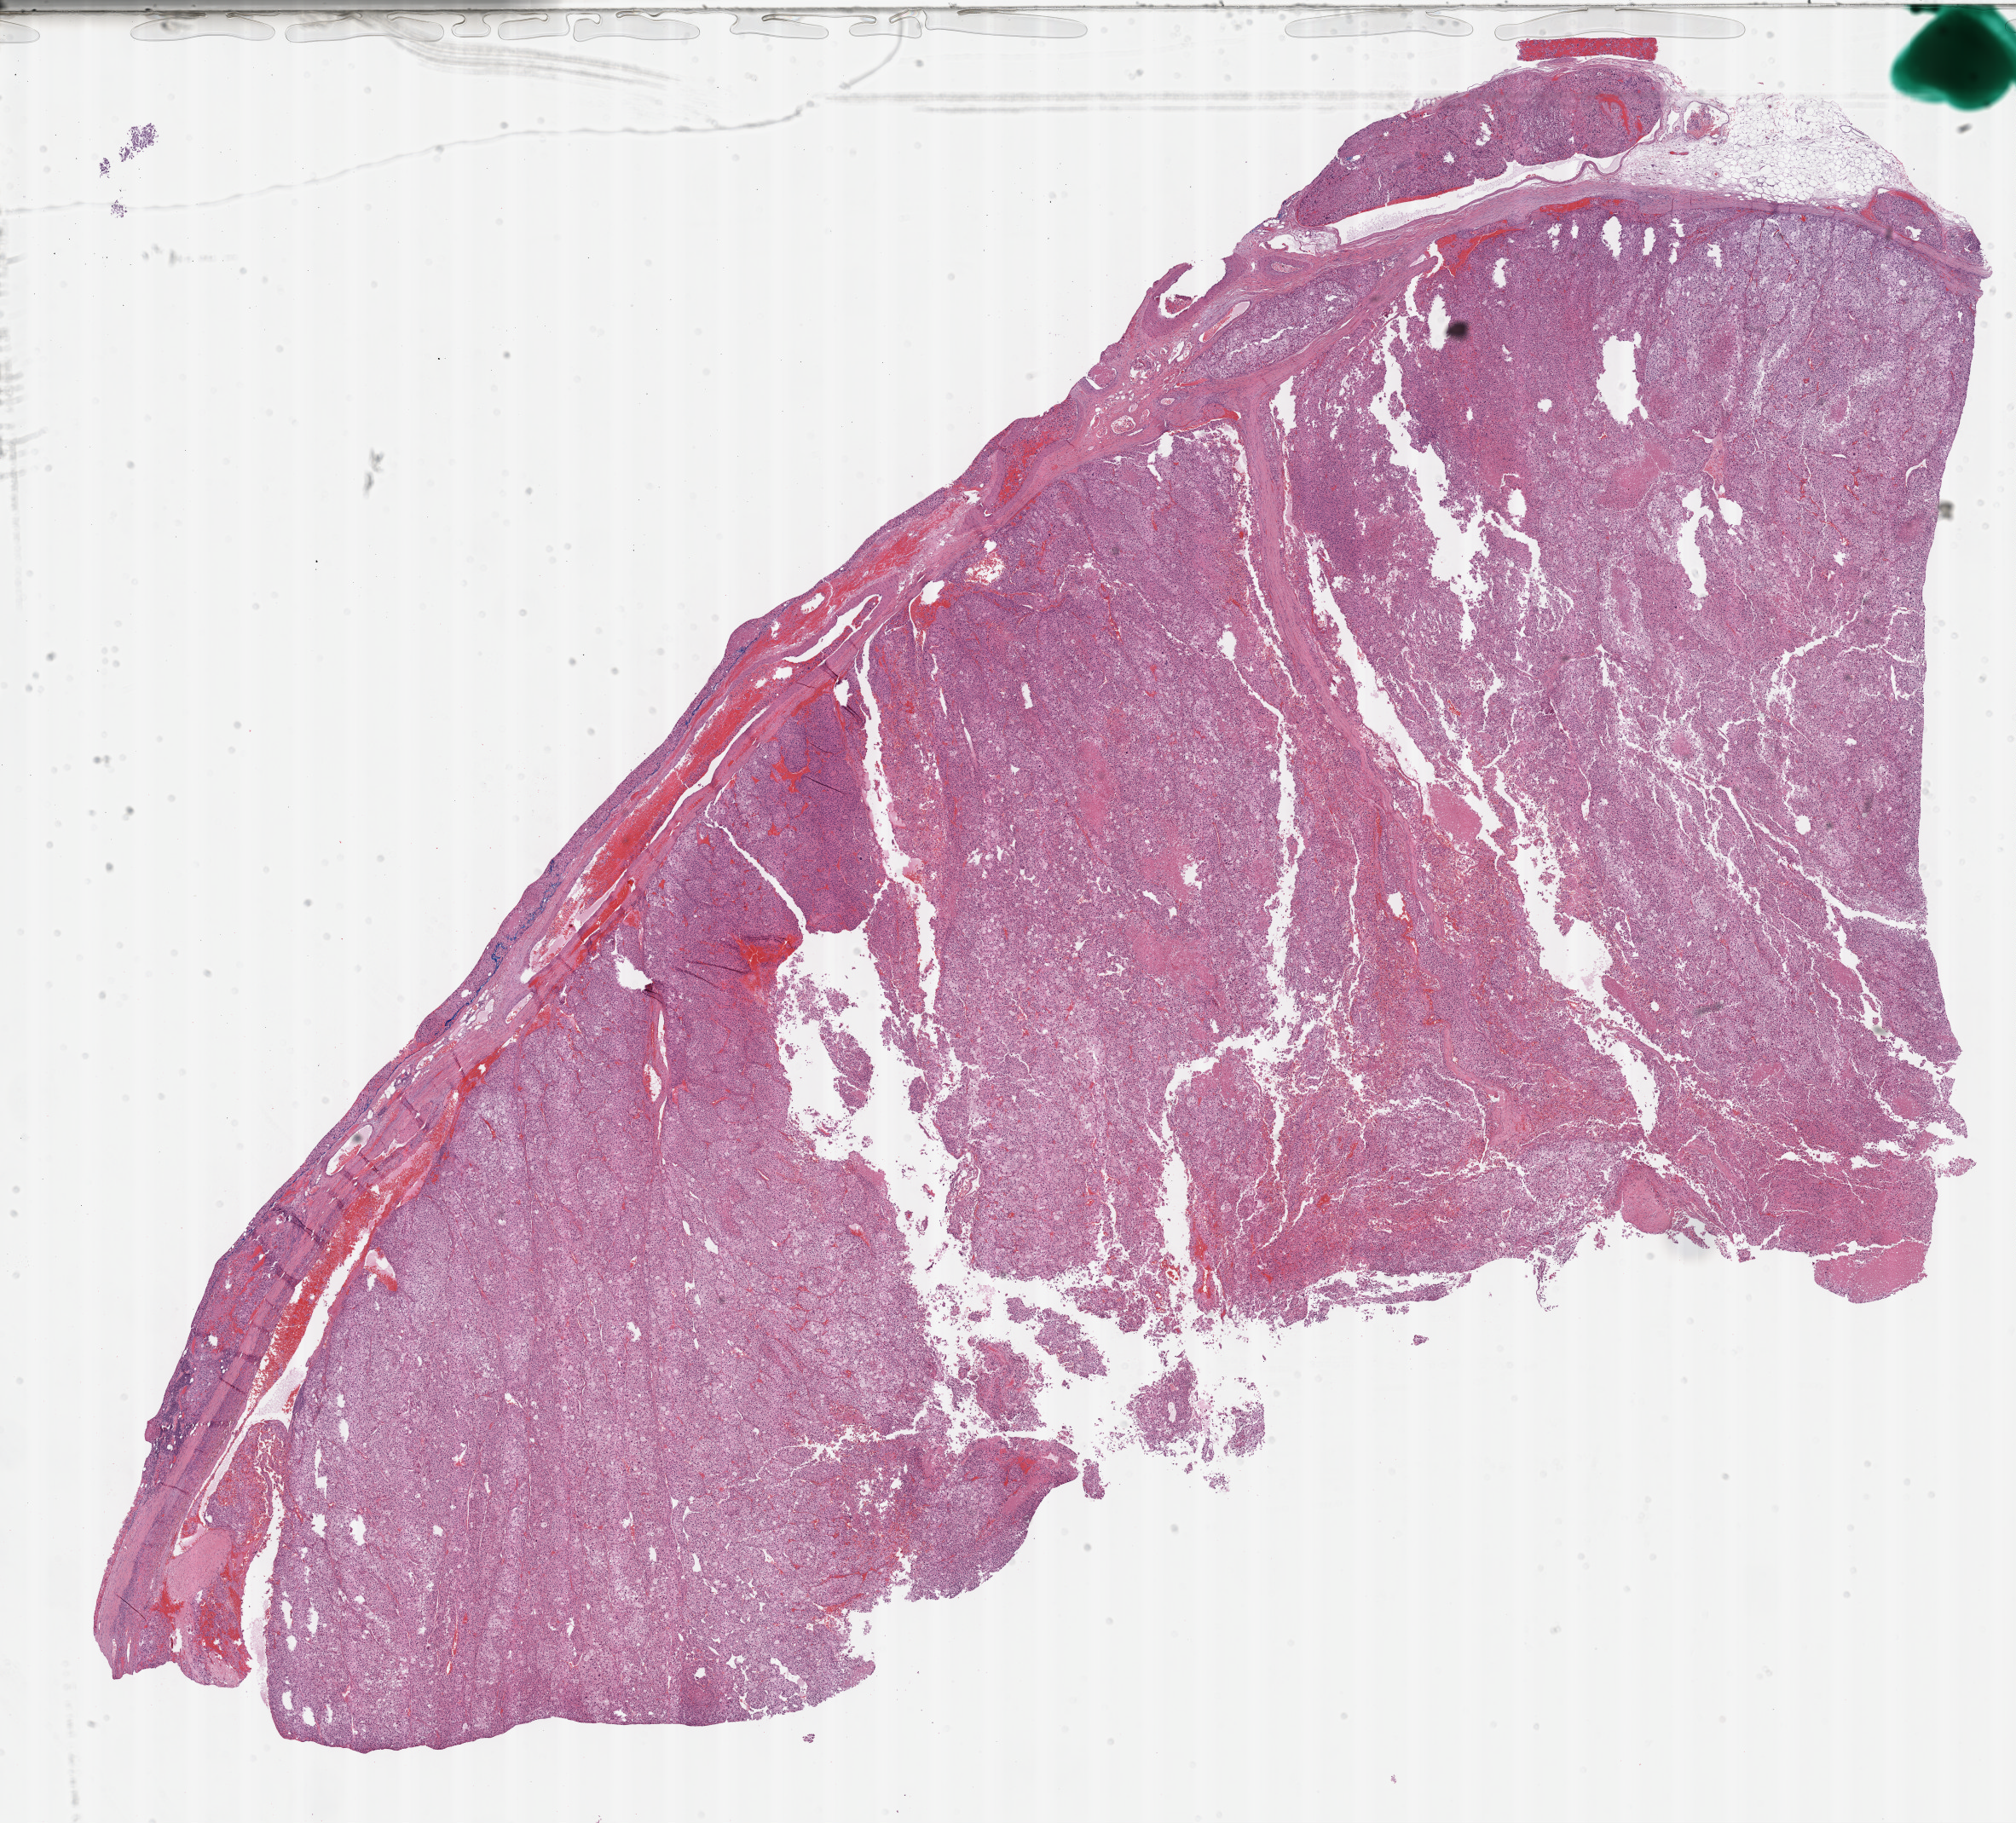
Hematoxylin and eosin (H&E) stained whole-slide image, whole scanned area (about 19.1 x 17.3 mm, slide scanned at 40x) shown as a low-resolution overview. Formalin-fixed paraffin-embedded (FFPE) diagnostic section. Sample: primary tumour, adrenal cortex. Patient: female, age at initial diagnosis 68 years.
Laterality: right. Lymph nodes positive (case pathology): 1 of 2 examined. Pathologic diagnosis: Adrenal cortical carcinoma (cortex of adrenal gland).